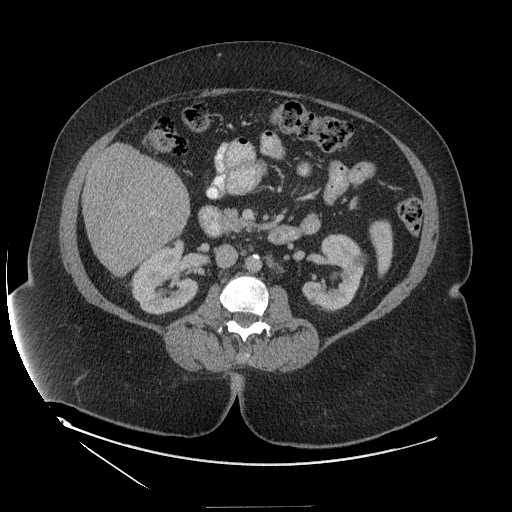
Contrast-enhanced abdominal CT (liver protocol), one axial slice; position 47 of 127 along the scan axis; reconstruction kernel STANDARD; 140 kVp; soft-tissue window (W 400 / L 40 HU); 512 × 512 image matrix, field of view 480 × 480 mm. Case-level facts recorded for this patient, not image findings: diagnosis: hepatocellular carcinoma (patient treated with transarterial chemoembolisation; whether this scan precedes or follows treatment is not stated here); TNM stage (as recorded): Stage-II.
Structures marked on this image (semi-automatically segmented with operator editing):
- liver parenchyma outside the tumour (the mass and vessels are separate outlines, so this box may not span the whole liver): bounding box <82,144,190,274> (left, top, right, bottom; pixels)
- liver vessels: <151,212,153,214>